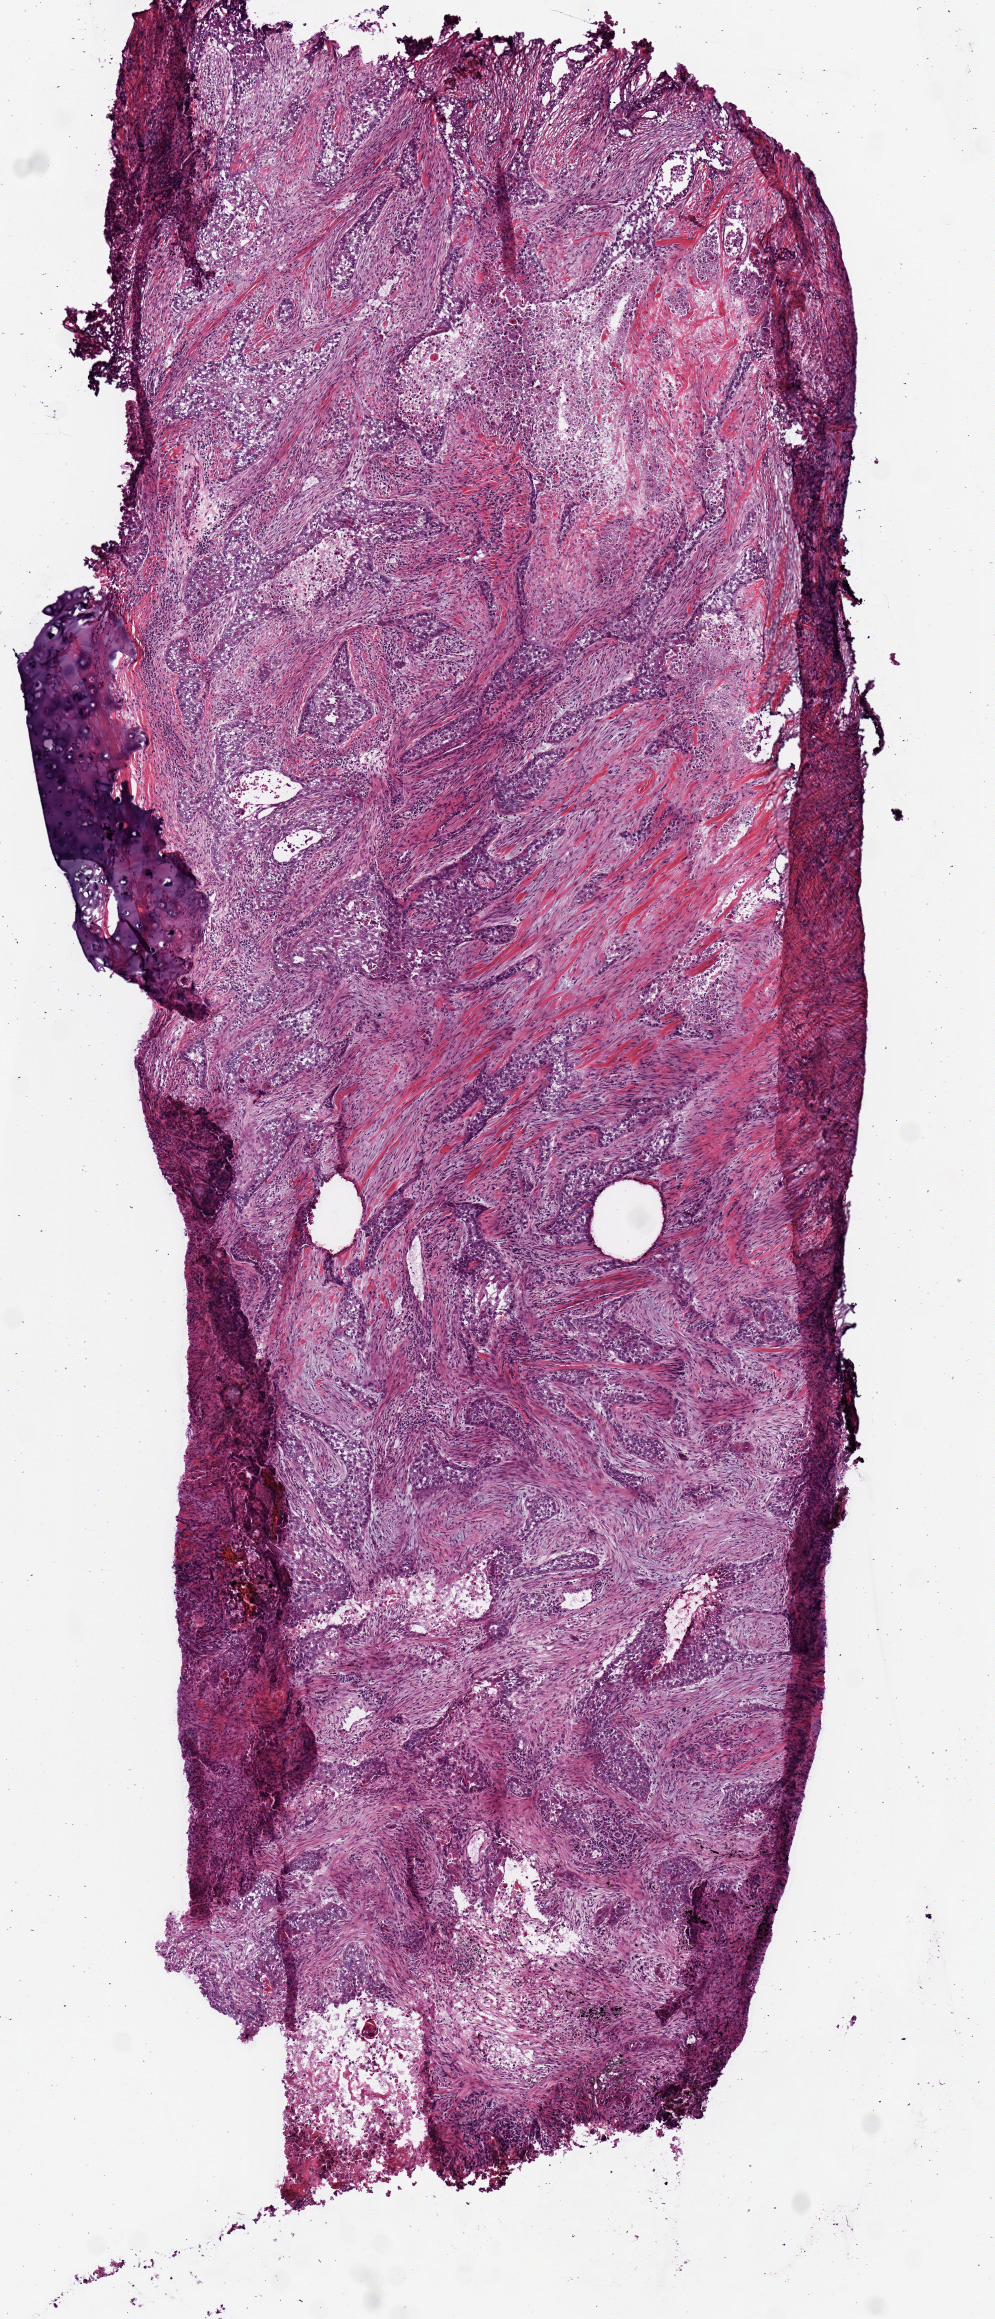
Whole-slide histology image, Hematoxylin and eosin (H&E) stained — a low-resolution overview of the entire scanned area, about 3.9 x 9.2 mm, frozen section, primary tumour sample from the lung. Male, age 73 years at initial diagnosis. Pathologist review of this section (percent, as recorded): tumour cells 52%, tumour nuclei 60%, normal cells 0%, stromal cells 40%, necrosis 8%.
• AJCC pathologic stage: IIIB (6th edition)
• TNM: T4 N1 M0
• histologic diagnosis: Squamous cell carcinoma, NOS